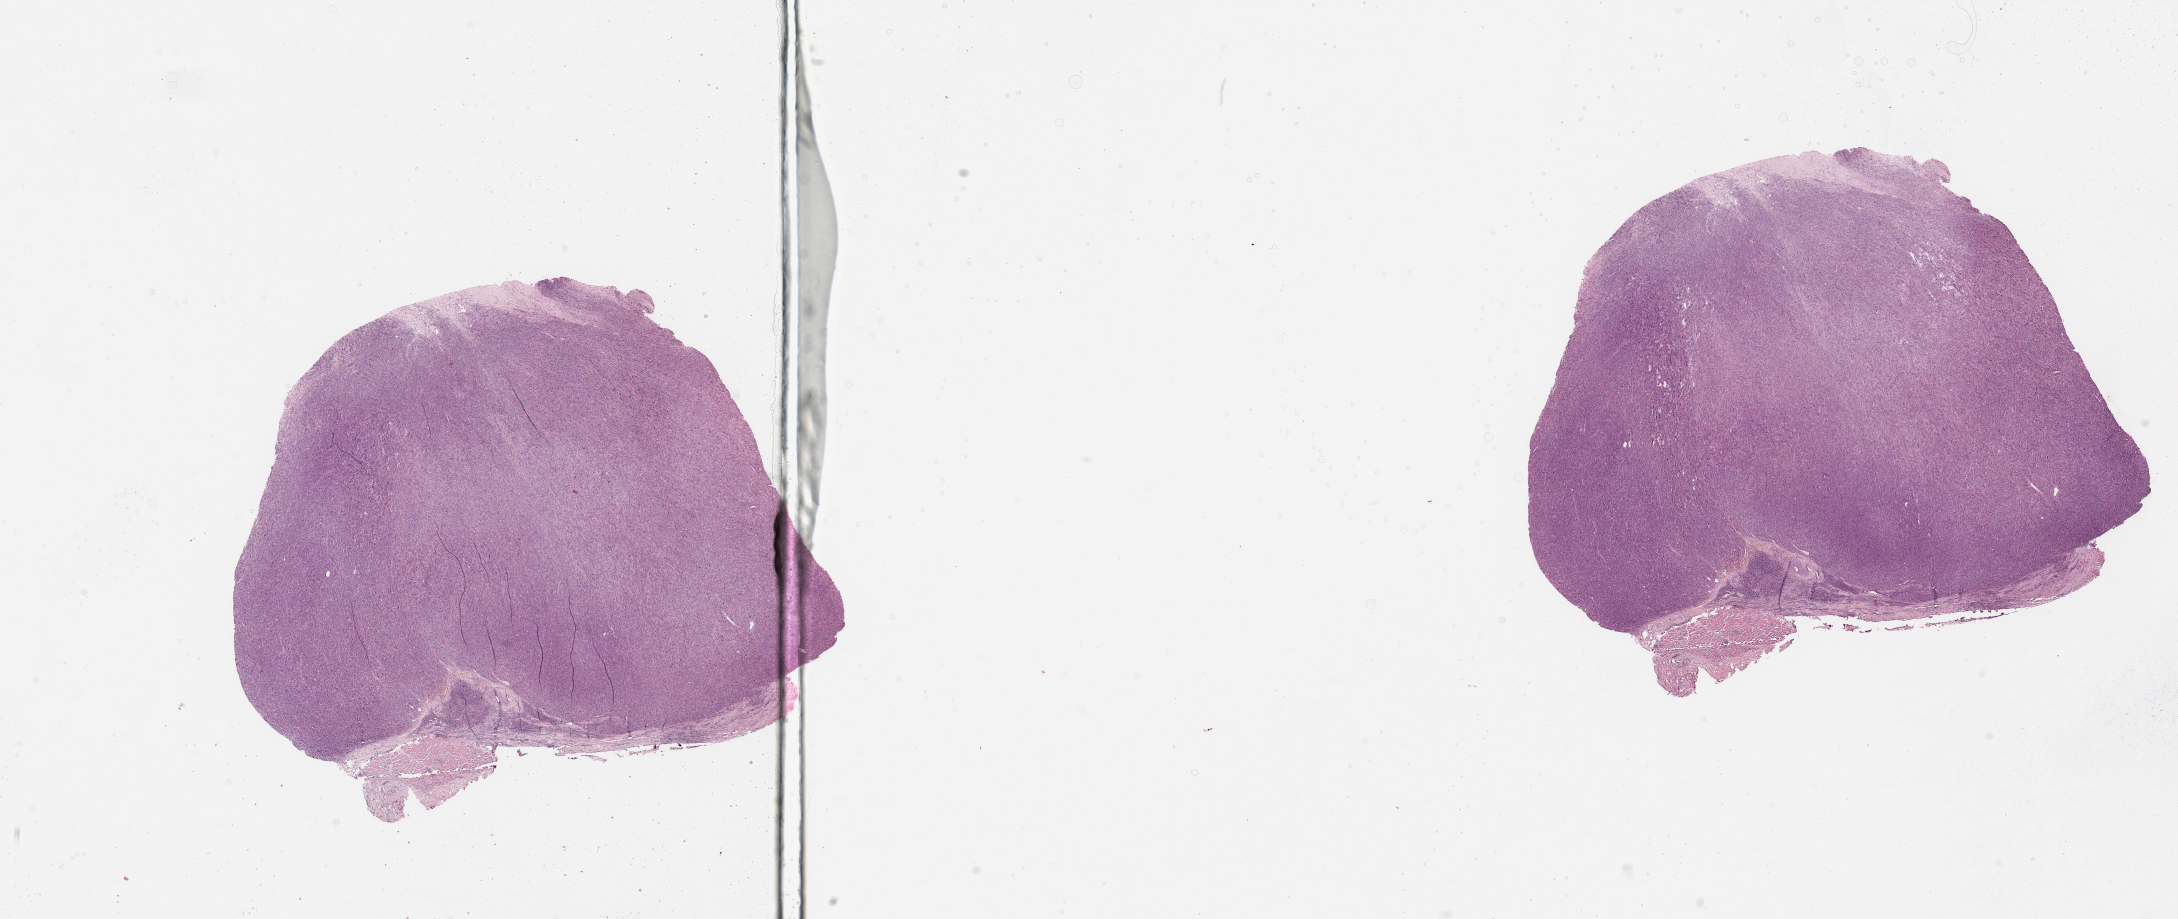
Hematoxylin and eosin (H&E) stained whole-slide image, whole scanned area (about 34.5 x 14.5 mm, from a 20x scan) shown as a low-resolution overview; tumour tissue sample. Patient: female, age 52 years.
Patient diagnosis (cohort enrolment): sarcoma (site not recorded at cohort level). Primary tumour site (as recorded): lower extremity.